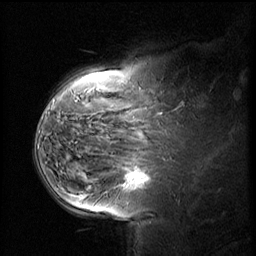
Breast MRI (dynamic contrast-enhanced), one sagittal slice; slice 41 of 58 in the series (ordered by position); dynamic contrast-enhanced series, image 2 of 2 at this slice position (ordered by acquisition); 1.5 T; TE 4.2 ms, TR 8.9 ms; 256 × 256 image matrix, field of view 220 × 220 mm. Female patient, age 37 years. Case-level facts recorded for this patient, not image findings: setting: breast cancer imaged before/during neoadjuvant chemotherapy; receptor status: triple-negative.
Outlined on this slice (semi-automatic segmentation, software-assisted and operator-edited):
- analysis volume of interest (the breast-tissue region the enhancement analysis was run in; not a lesion): bounding box [x1, y1, x2, y2] px = [114, 160, 166, 207]
- tumour enhancement mask (voxels above the 140 % enhancement threshold inside the analysis volume of interest): [125, 174, 147, 187]